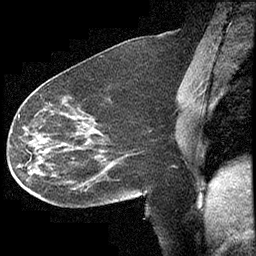
Breast MRI (dynamic contrast-enhanced), one sagittal slice. Slice 172 of 232 in the series (ordered by position). Dynamic contrast-enhanced study with each time point stored as its own series, time point 2 of 4 at this slice position (early post-contrast, ordered by acquisition time). 1.5 T. TE 4.2 ms, TR 6.7 ms. 3 mm slice thickness. 256 × 256 image matrix, field of view 200 × 200 mm. Female patient, age 63 years. From the clinical record (not read from this slice): setting: breast cancer imaged before/during neoadjuvant chemotherapy; receptor status: triple-negative.
Outlined on this slice (semi-automatic segmentation, software-assisted and operator-edited):
- analysis volume of interest (the breast-tissue region the enhancement analysis was run in; not a lesion): bounding box <13,90,140,208> (left, top, right, bottom; pixels)
- tumour enhancement mask (voxels above the 70 % enhancement threshold inside the analysis volume of interest): <18,115,80,161>